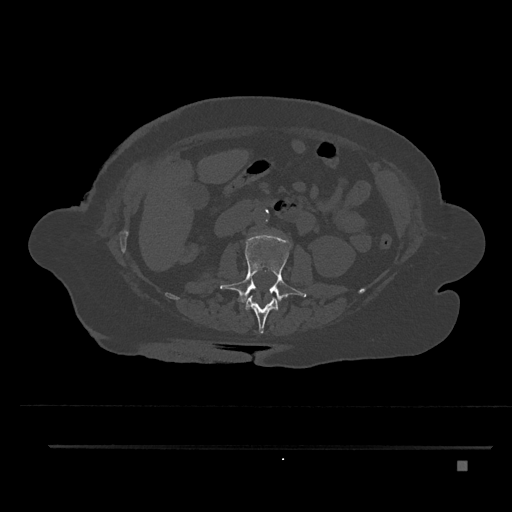
CT including the spine, one axial slice. Position 181 of 797 along the scan axis. Reconstruction kernel Br40s/3. Bone window (W 1800 / L 400 HU). 0.5 mm slice thickness. 512 × 512 image matrix, field of view 437 × 437 mm. Female patient, age 76 years. Case-level facts recorded for this patient, not image findings: primary cancer: lung; vertebrae with lytic lesions (as recorded): T11, L3.
Annotated regions visible in this slice (semi-automatic segmentation, software-assisted and operator-edited):
- L1 vertebra: box from (x=245, y=296) to (x=279, y=334) px
- L2 vertebra: (x=220, y=235)–(x=307, y=303)